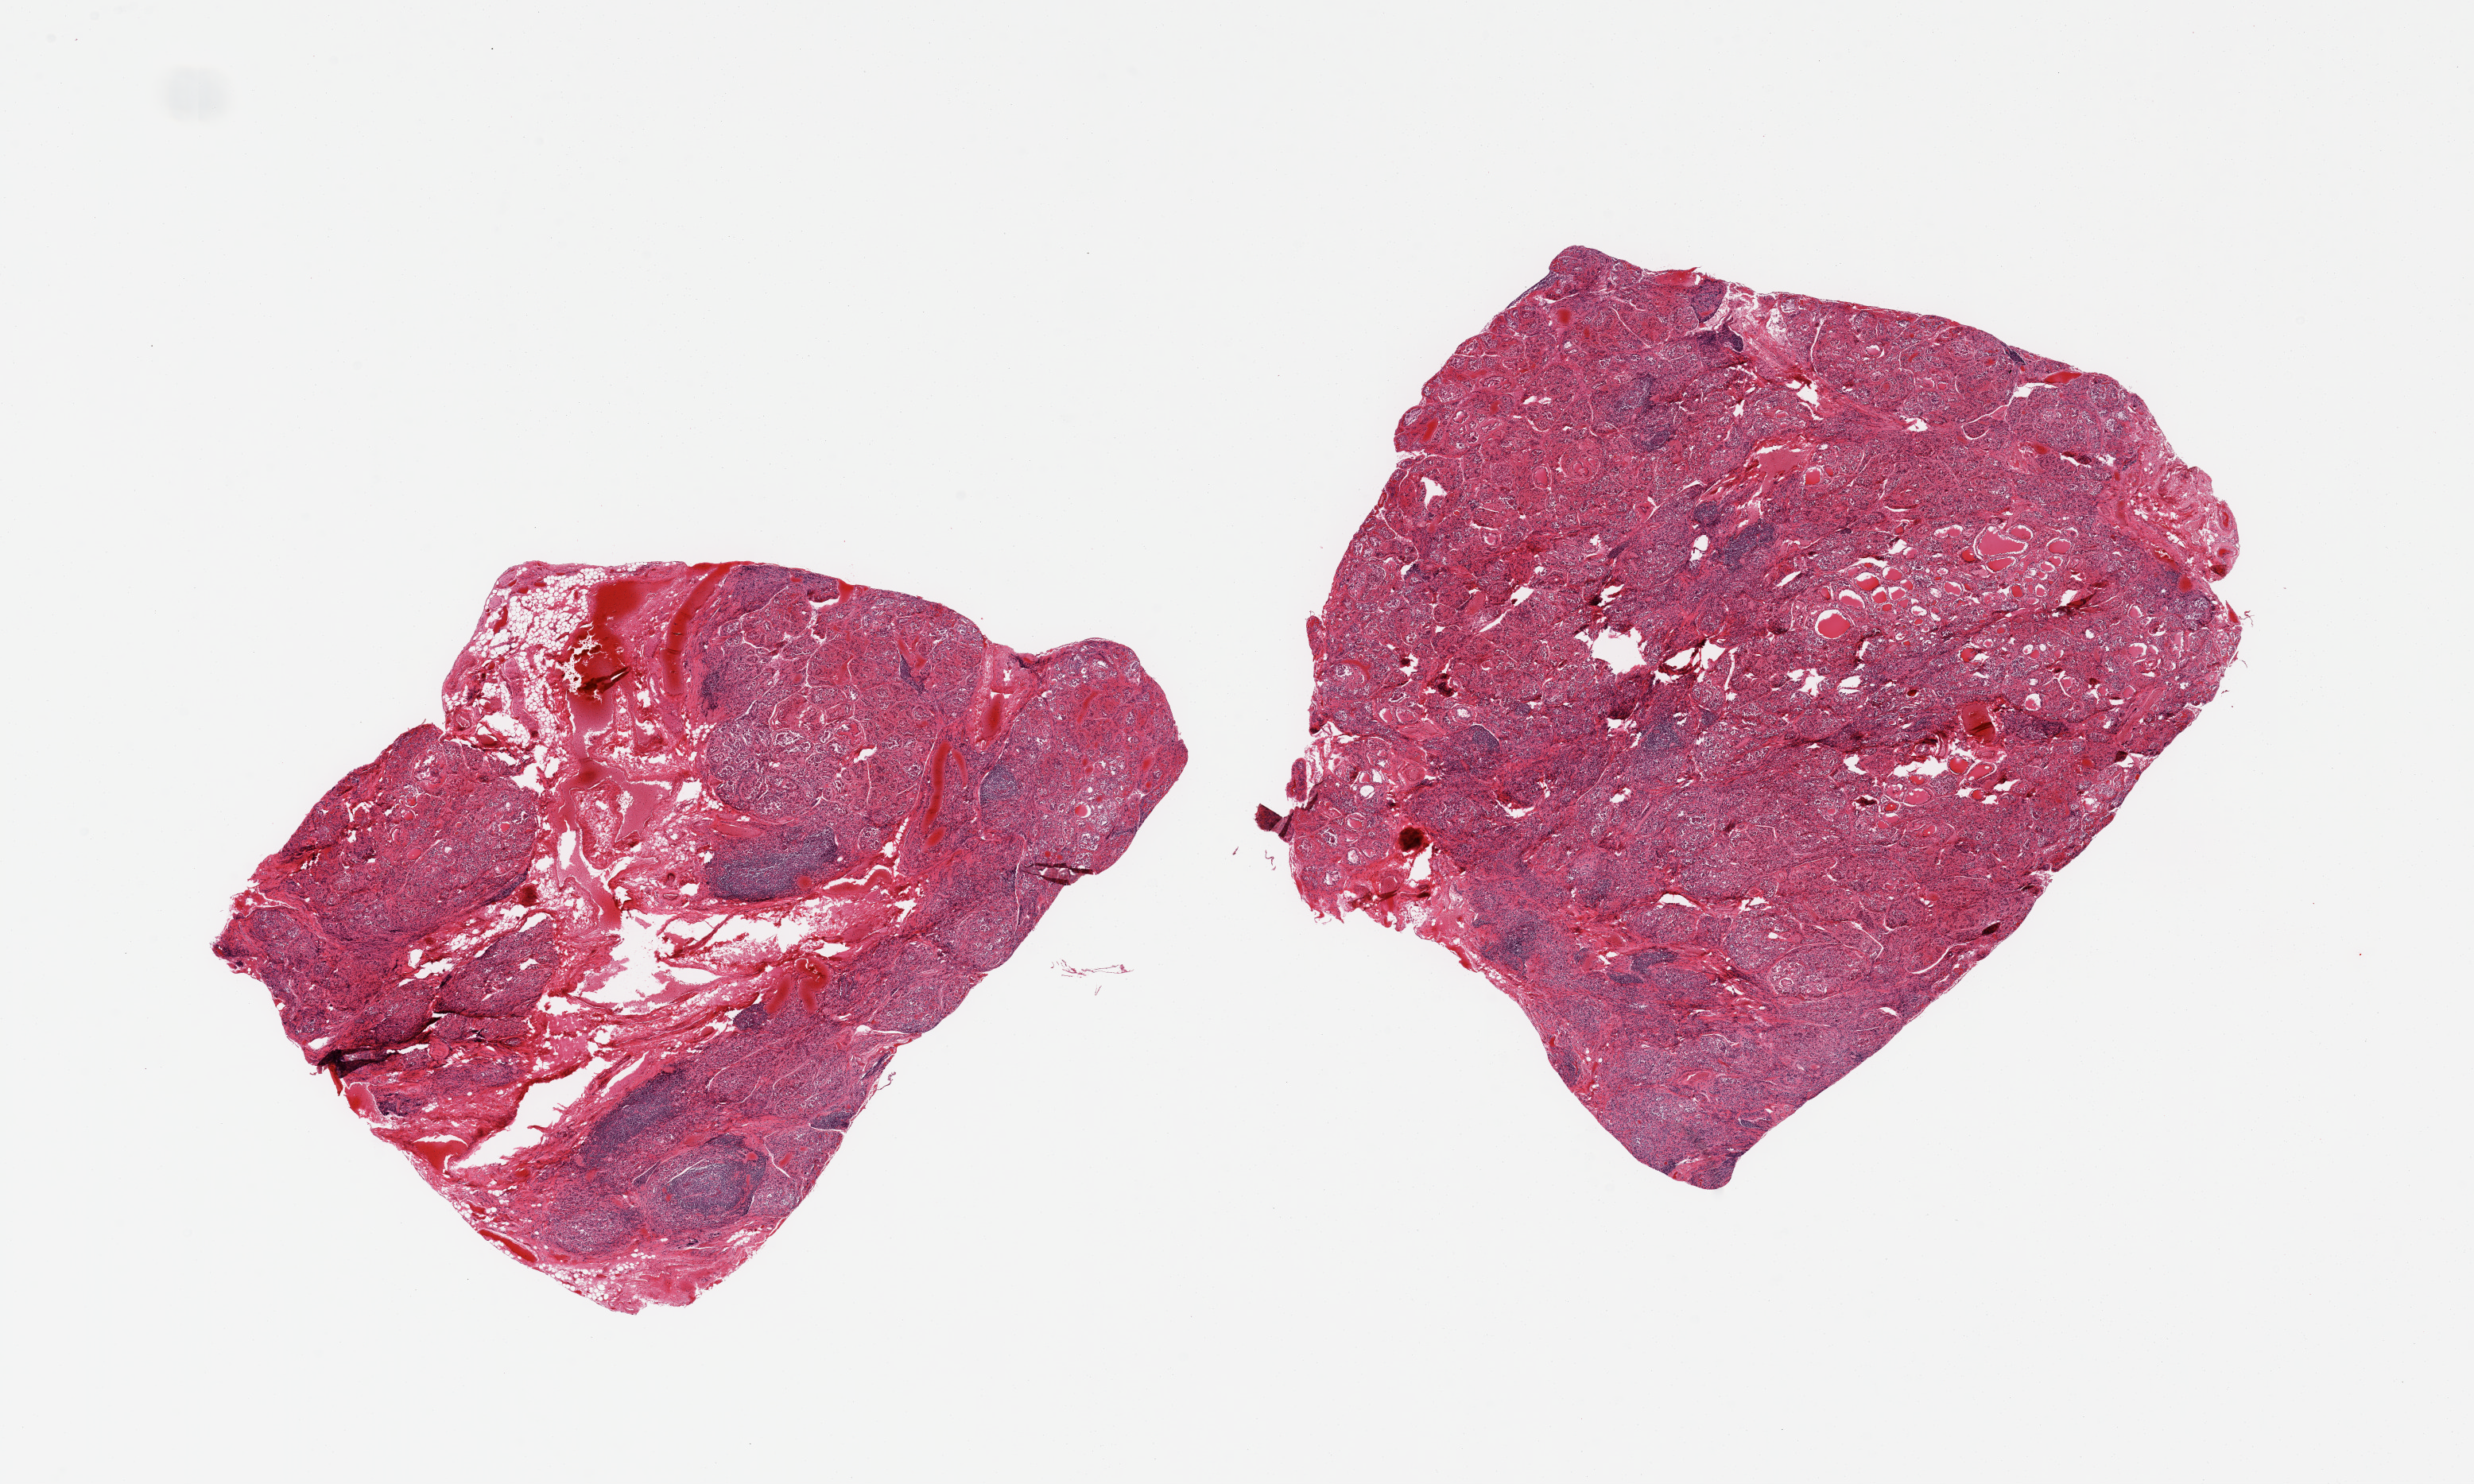
Digitized haematoxylin and eosin-stained section — low-resolution overview of the scanned area, about 24.6 x 14.8 mm (acquisition: 20x scan); PAXgene-fixed, paraffin-embedded tissue; target tissue: thyroid; tissue donor sample. Donor: male.
Pathologist's review note for this sample: 2 pieces; severe lymphocytic thyroiditis (Hashimoto).